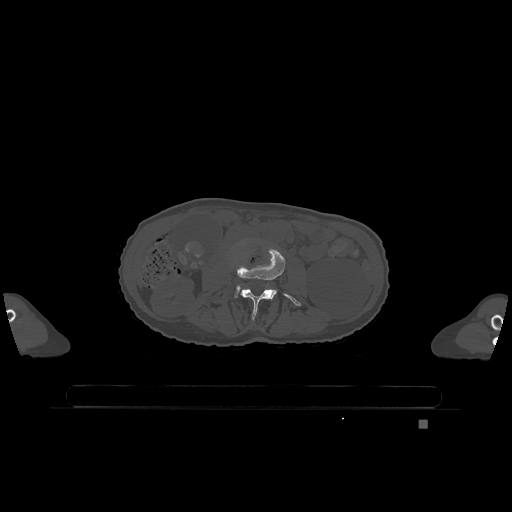
CT including the spine, one axial slice. Bone window (W 1800 / L 400 HU). 0.5 mm slice thickness. 512 × 512 image matrix. Female patient, age 74 years. From the clinical record (not read from this slice): primary cancer: lung.
Structures marked on this image (semi-automatic segmentation, software-assisted and operator-edited):
- L3 vertebra: bounding box (x1, y1, x2, y2) in pixels: (236, 247, 301, 319)
- L4 vertebra: (235, 287, 239, 298)